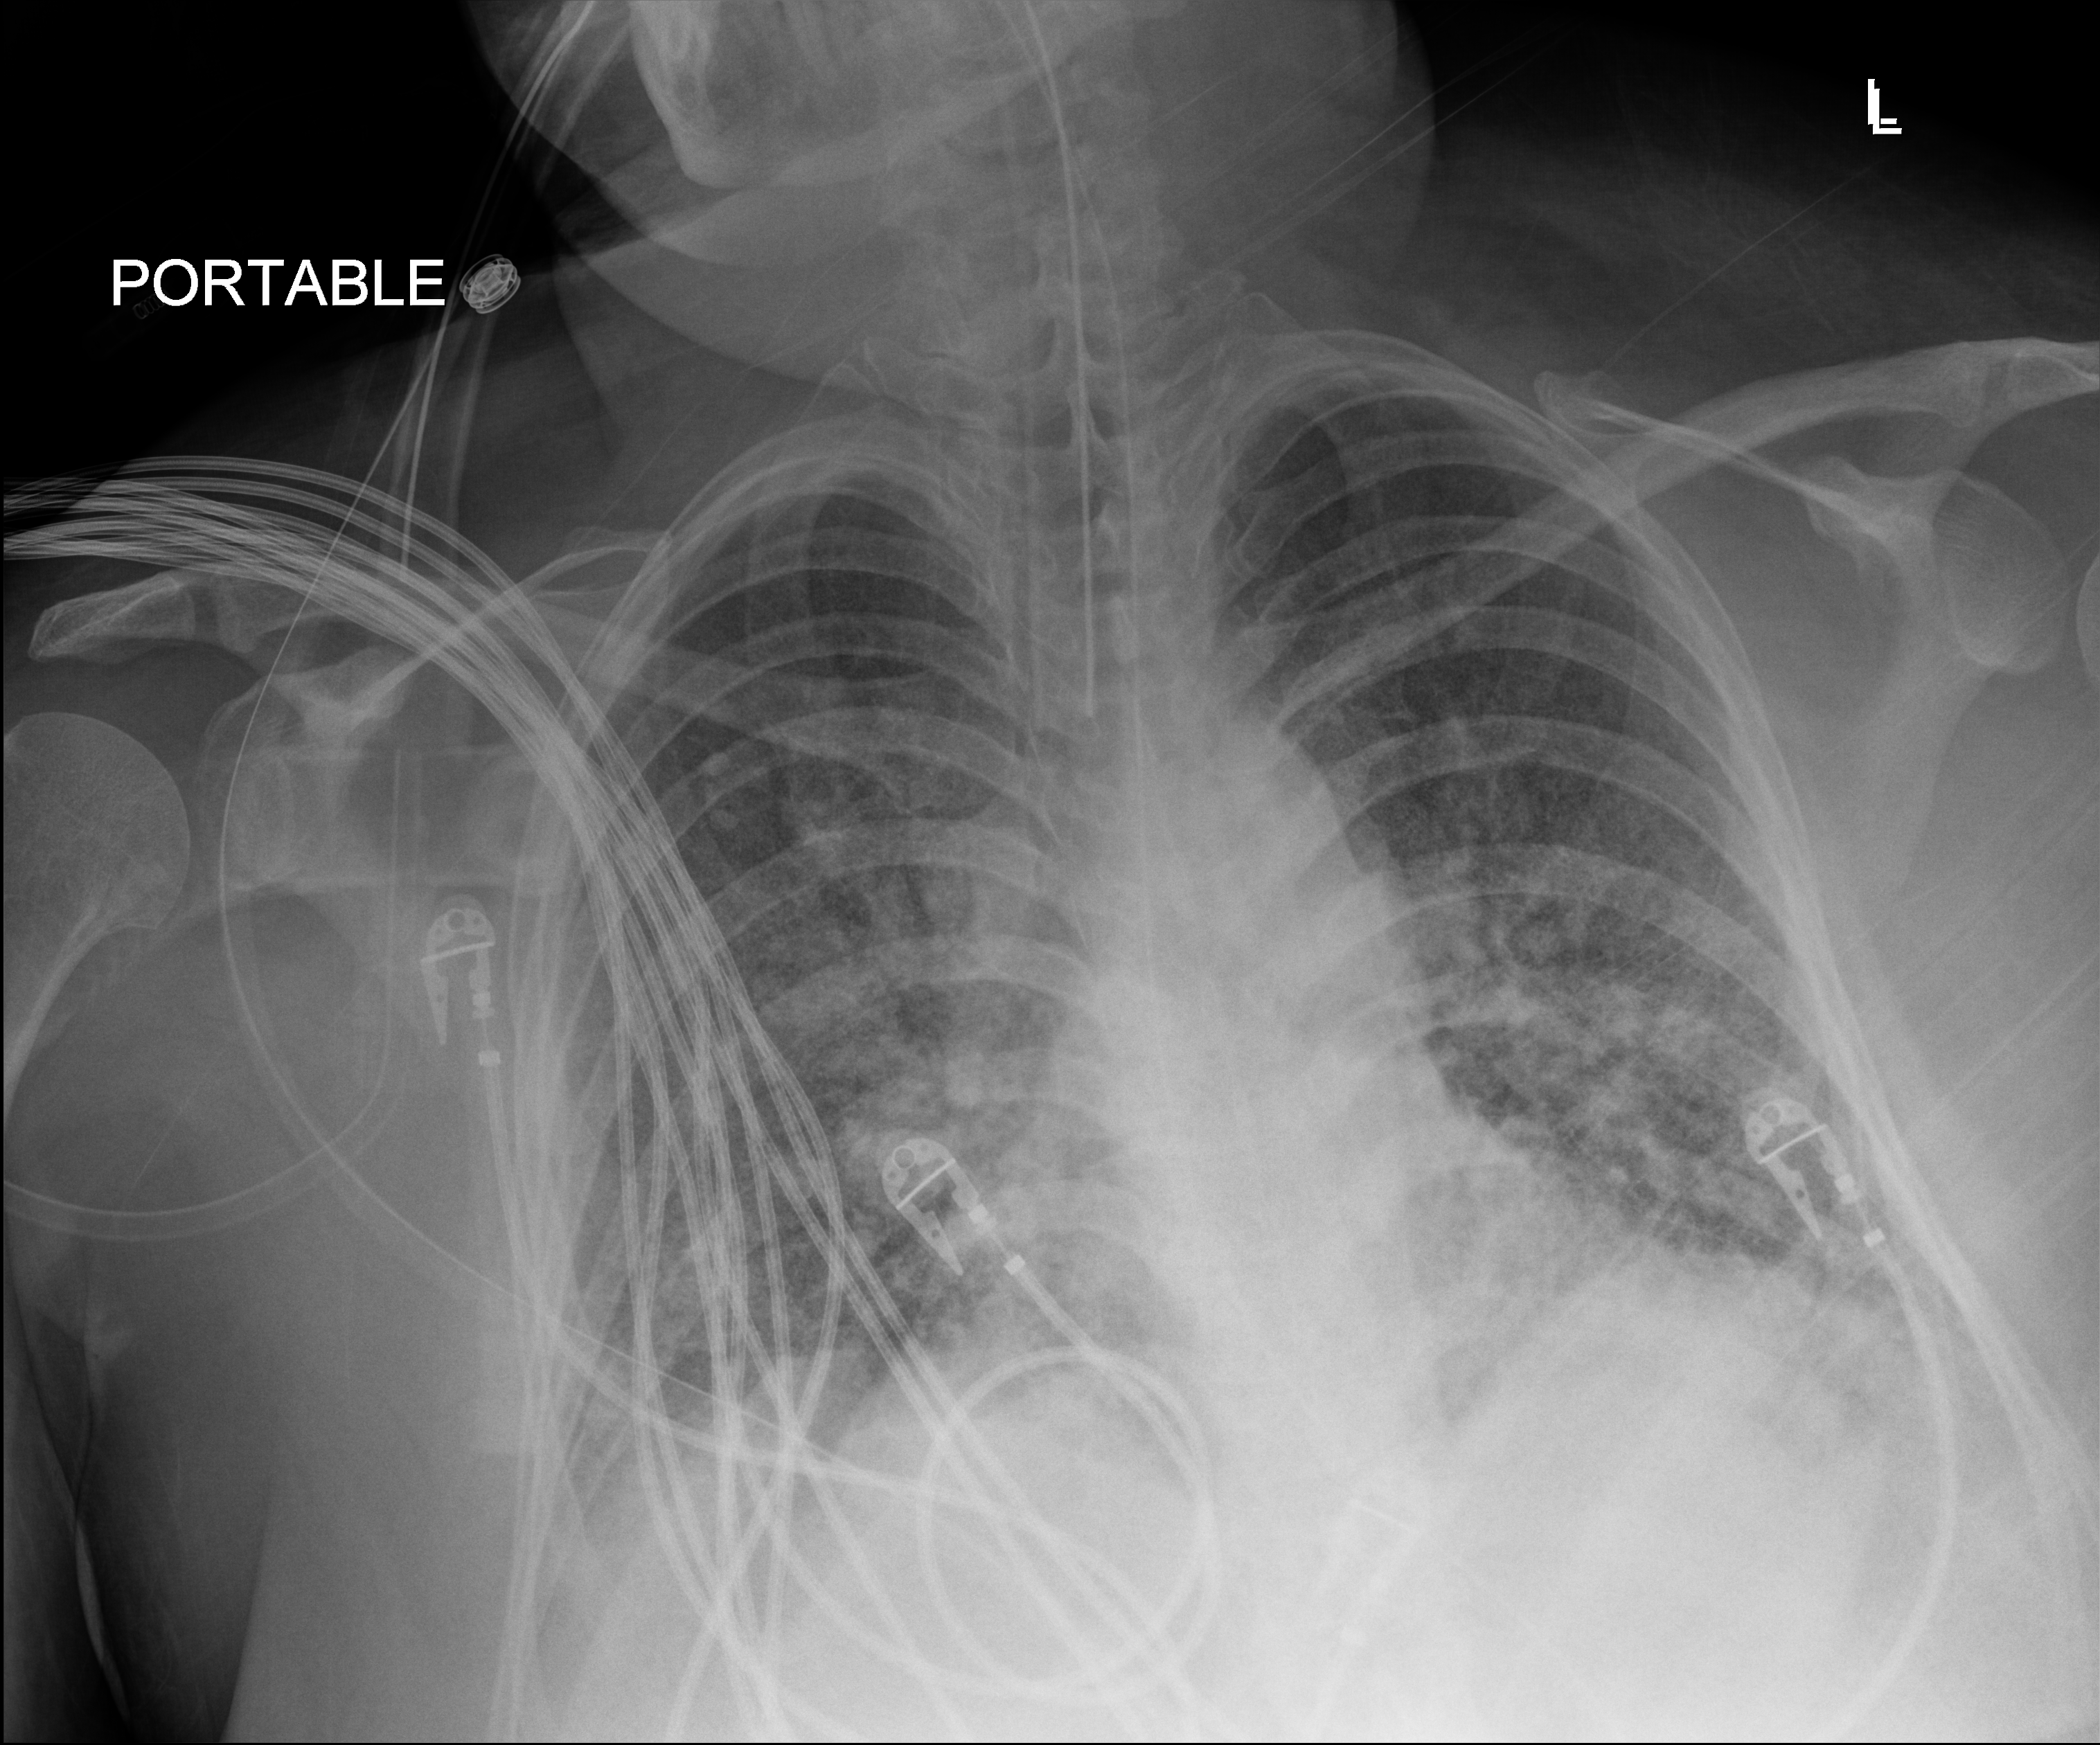
Portable chest radiograph. Patient hospitalised with COVID-19, aged 18–59 years.
Hospital-stay facts (about this admission, not read from this image; timing relative to this image not recorded): length of hospital stay: 48 days; mechanically ventilated during this hospital stay: yes.